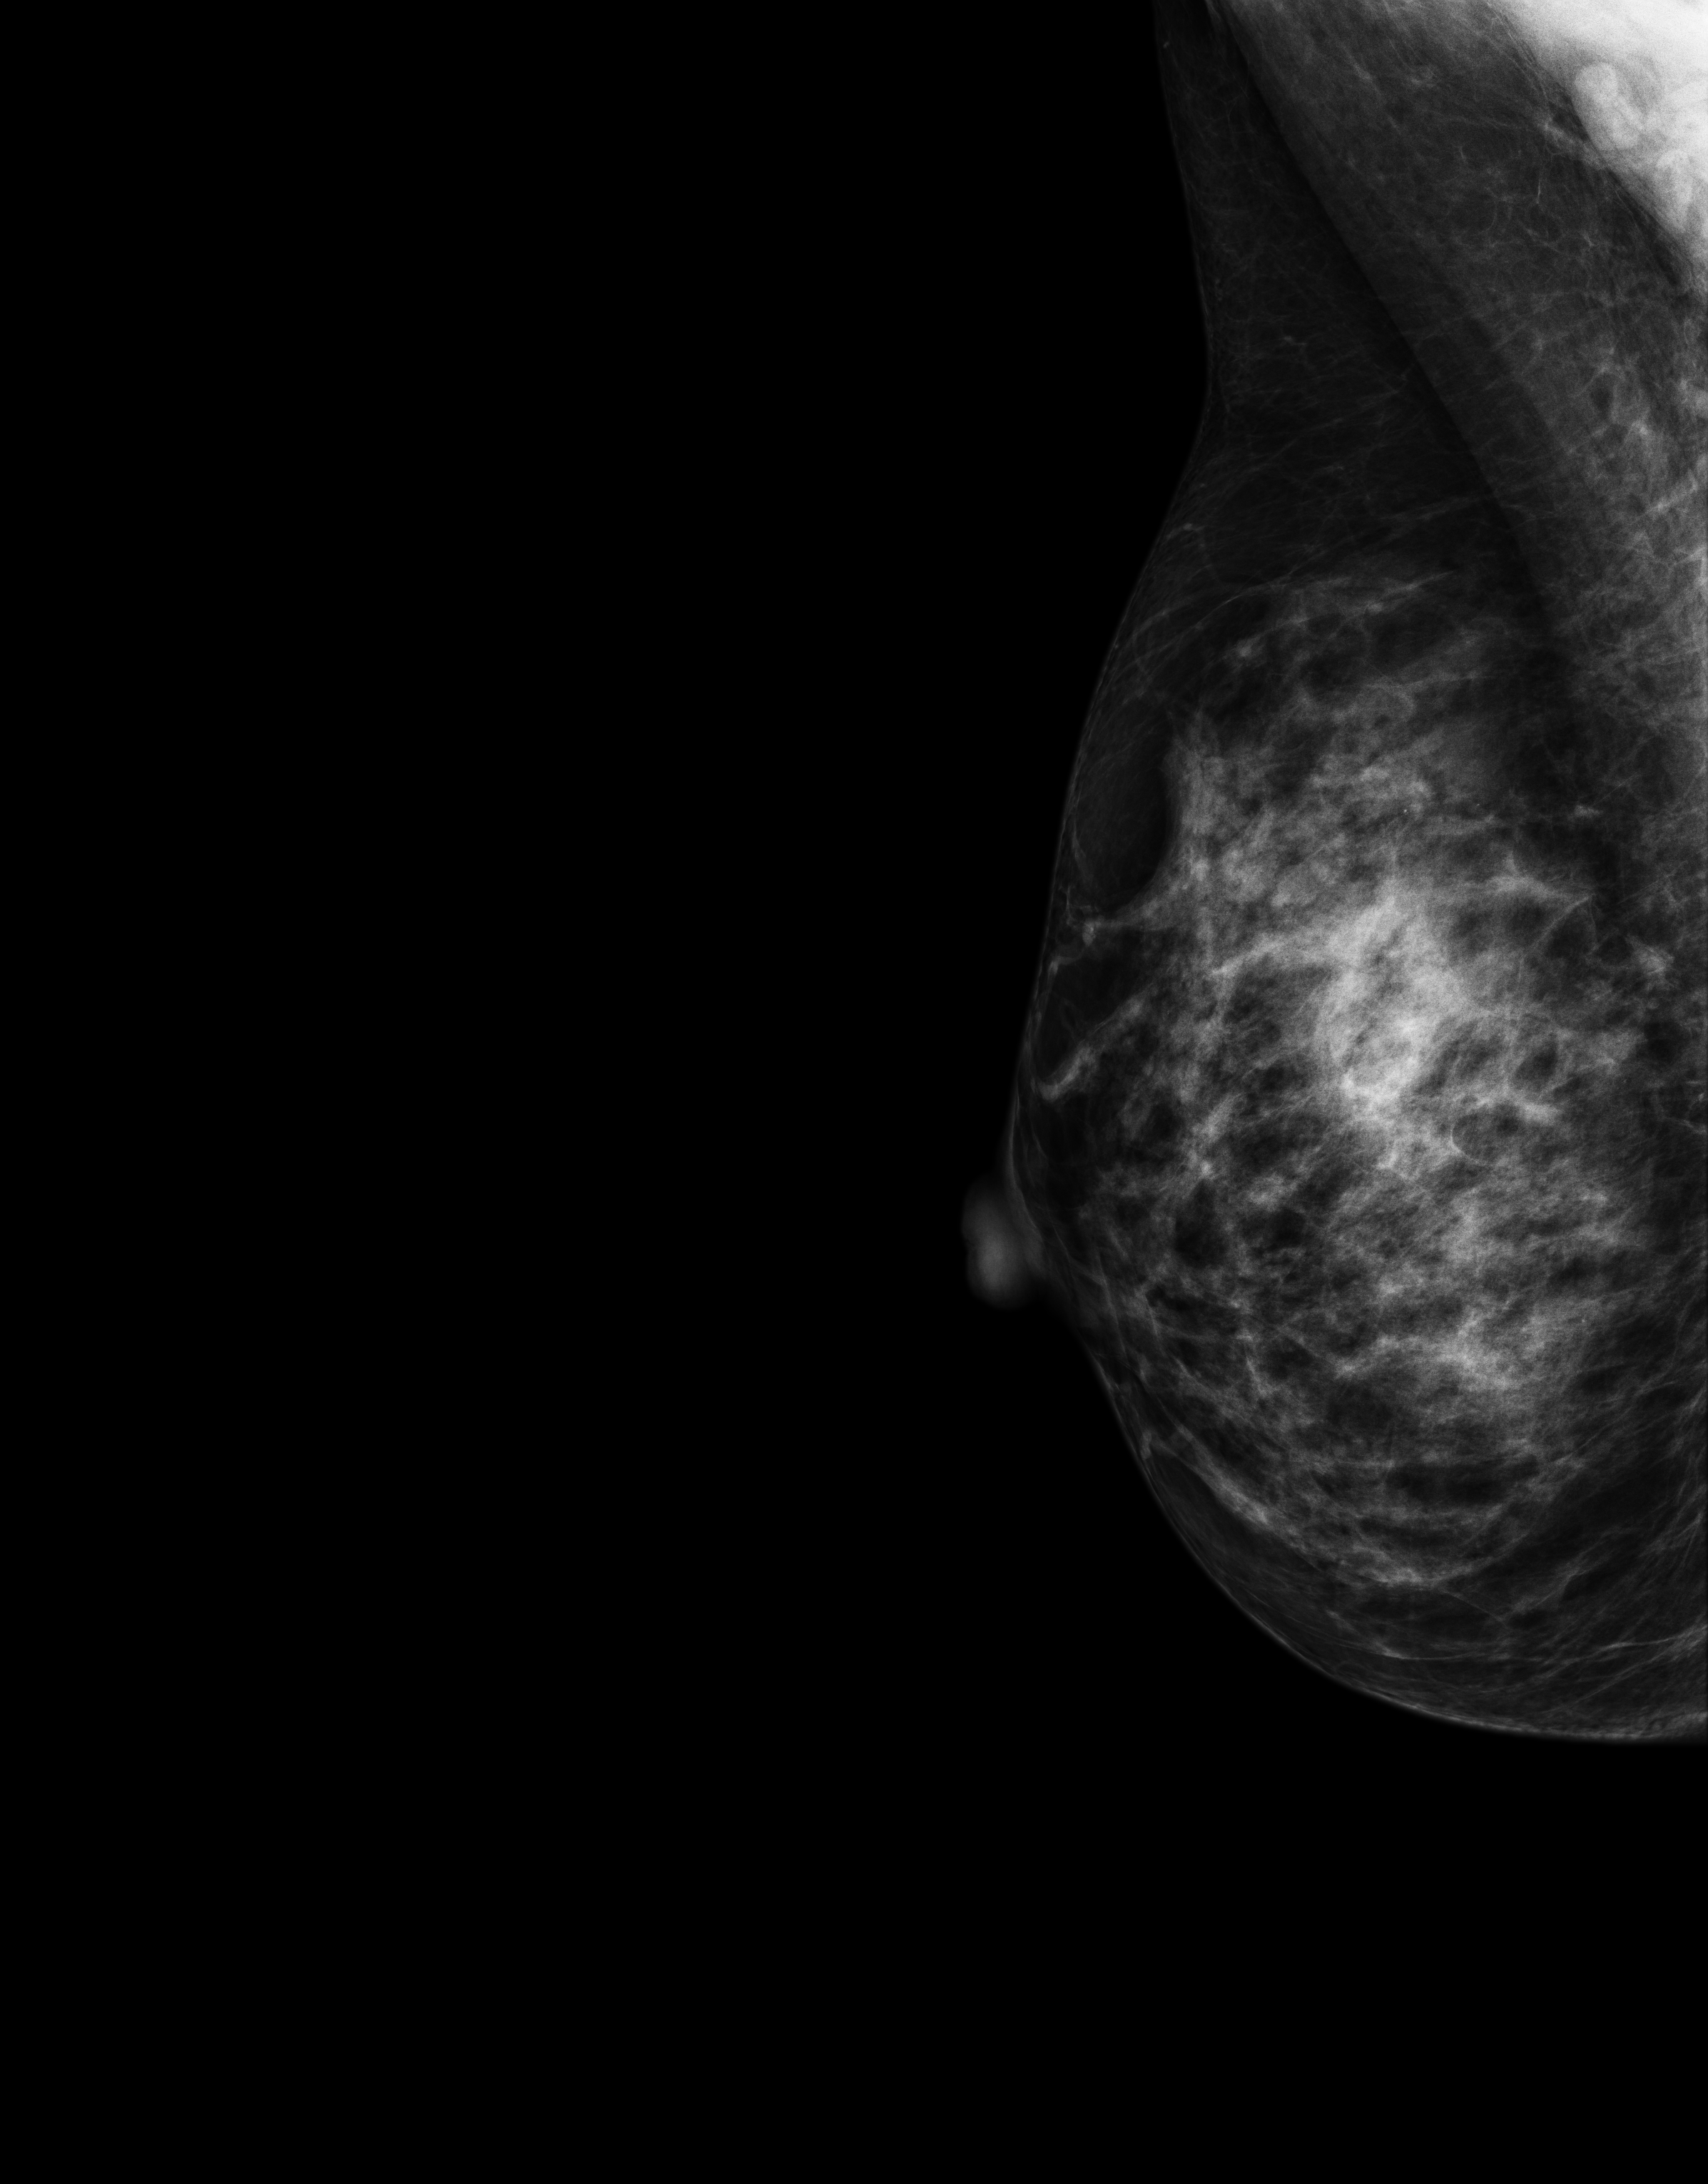
Digital mammogram (FFDM), right breast, medio-lateral oblique projection, screening examination, system: Senographe Essential ADS_56.21.3. Patient aged 42 years (female).
Breast density at the screening exam (both breasts): extremely dense (BI-RADS density category d). Final BI-RADS assessment for this screening round (tomosynthesis exam, both breasts): category 1. Recall: no recall after this screen.